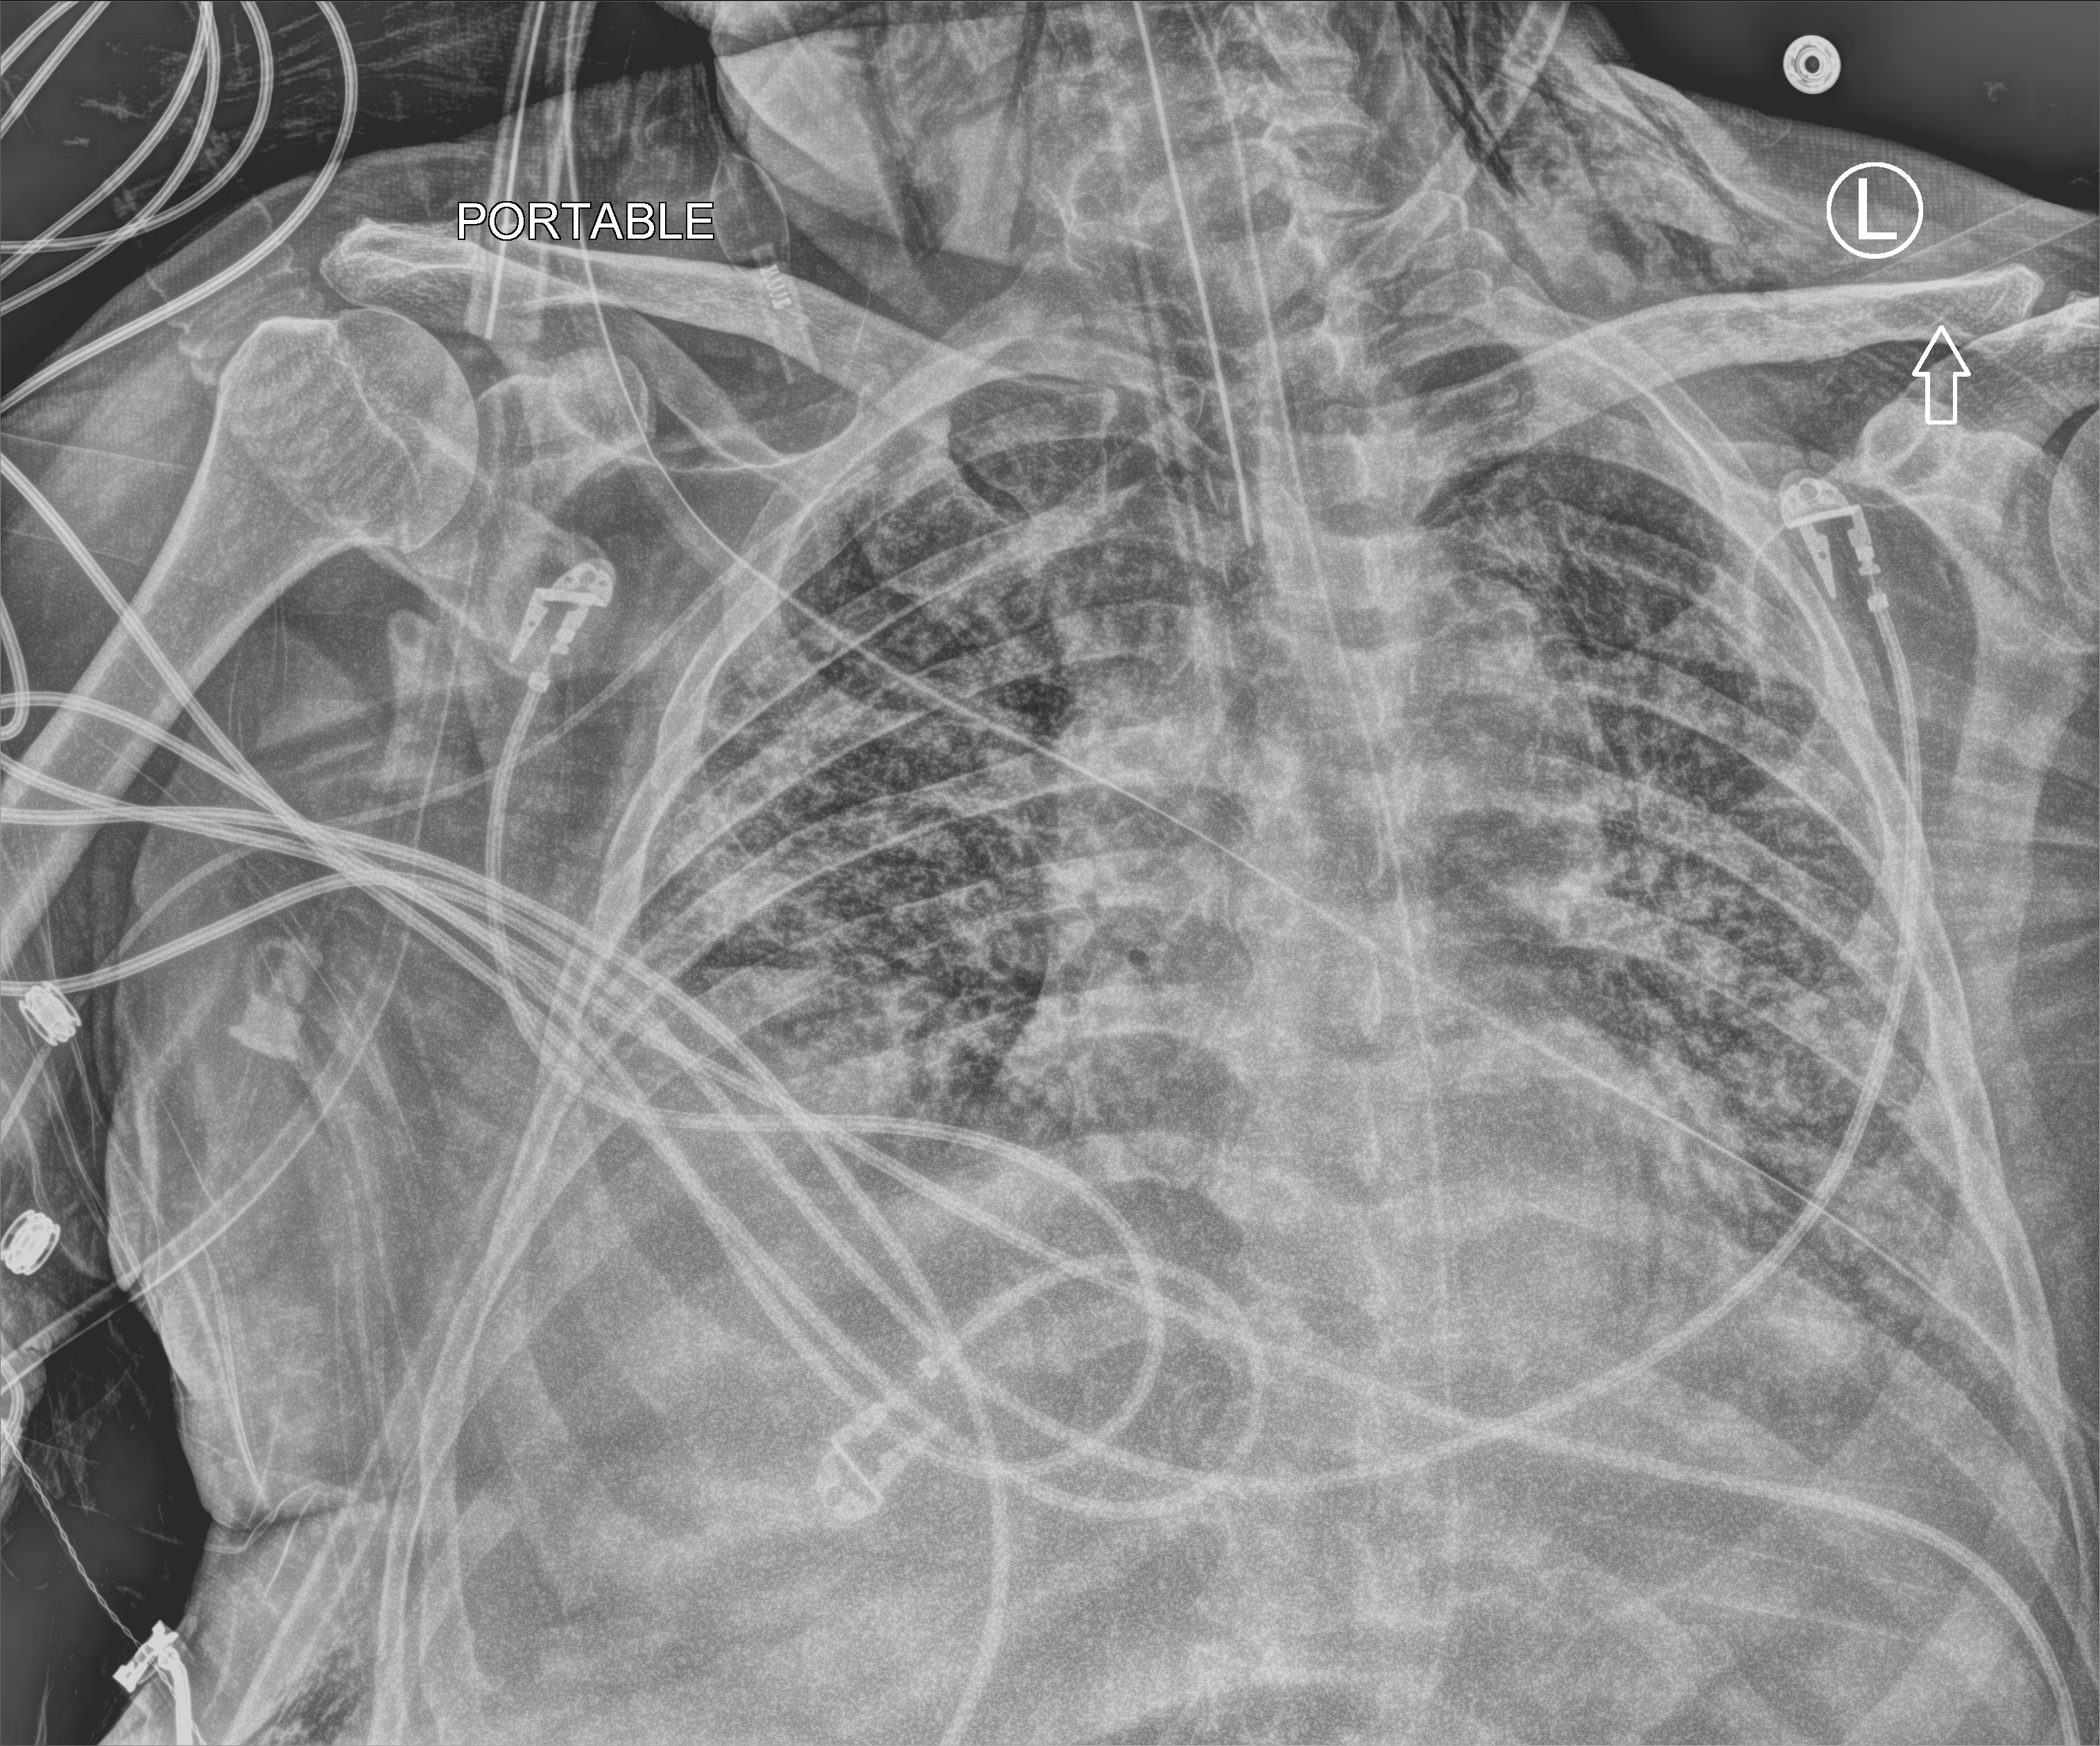
Chest X-ray (portable); anteroposterior (AP) projection. Male patient hospitalised with COVID-19, age 60–74 years.
Hospital-stay facts (about this admission, not read from this image; timing relative to this image not recorded):
- COPD (admission record): no